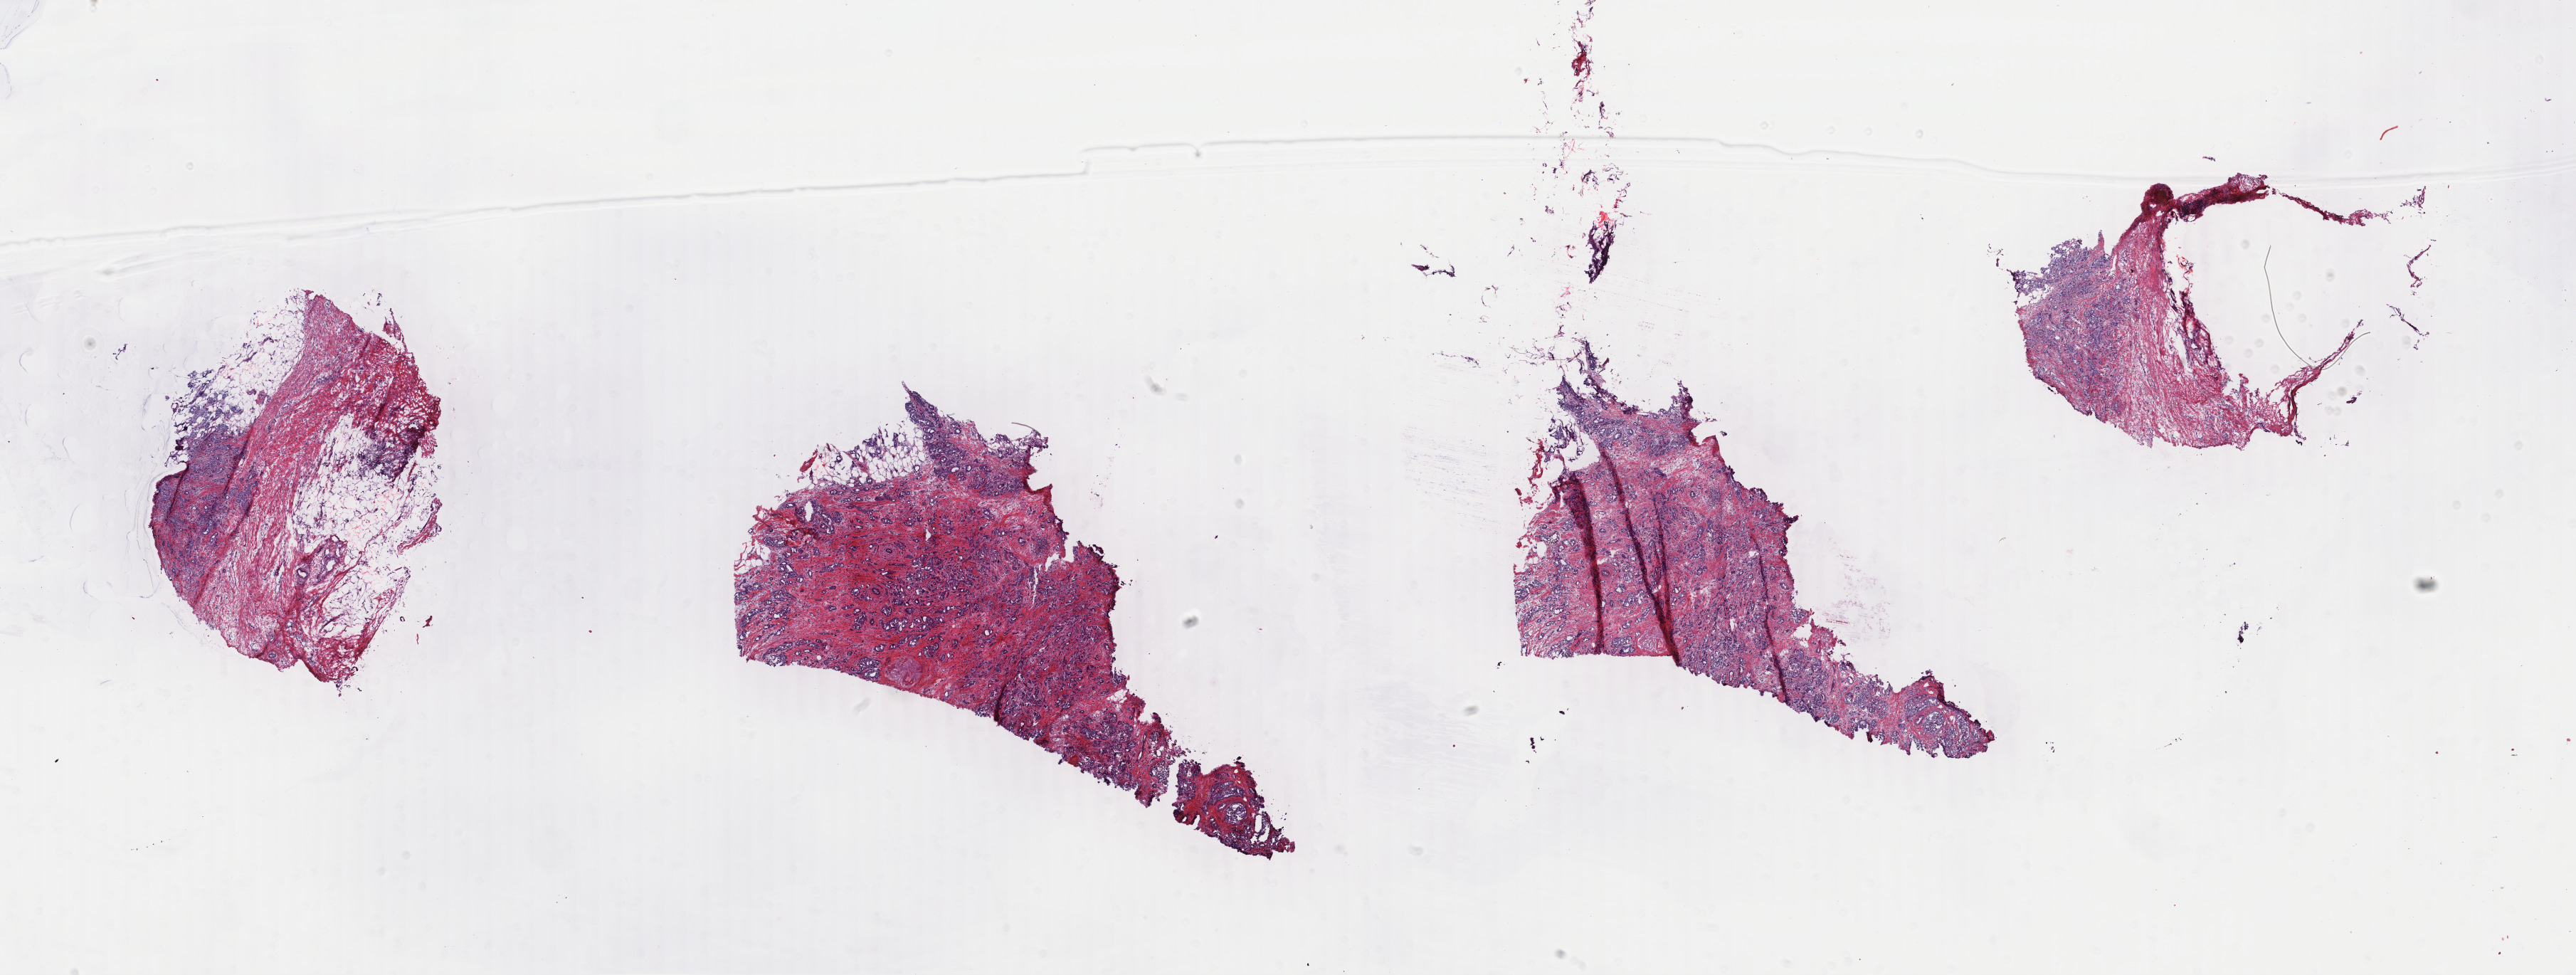
Whole-slide histology image, Hematoxylin and eosin (H&E) stained, whole scanned area (about 28.8 x 10.9 mm) shown as a low-resolution overview; frozen section from the bottom of the tissue portion; breast, primary tumour sample. Patient: female, age at initial diagnosis 68 years. Composition of this section per pathologist review: tumour cells 75%, tumour nuclei 75%, normal cells 1%, stromal cells 24%, necrosis 0%. Infiltration values recorded for this section: lymphocyte infiltration 2%, monocyte infiltration 0%, neutrophil infiltration 0%.
• lymph nodes positive (case pathology): 2 of 14 examined
• AJCC pathologic stage: IIA
• diagnosis: Infiltrating duct carcinoma, NOS
• laterality: left